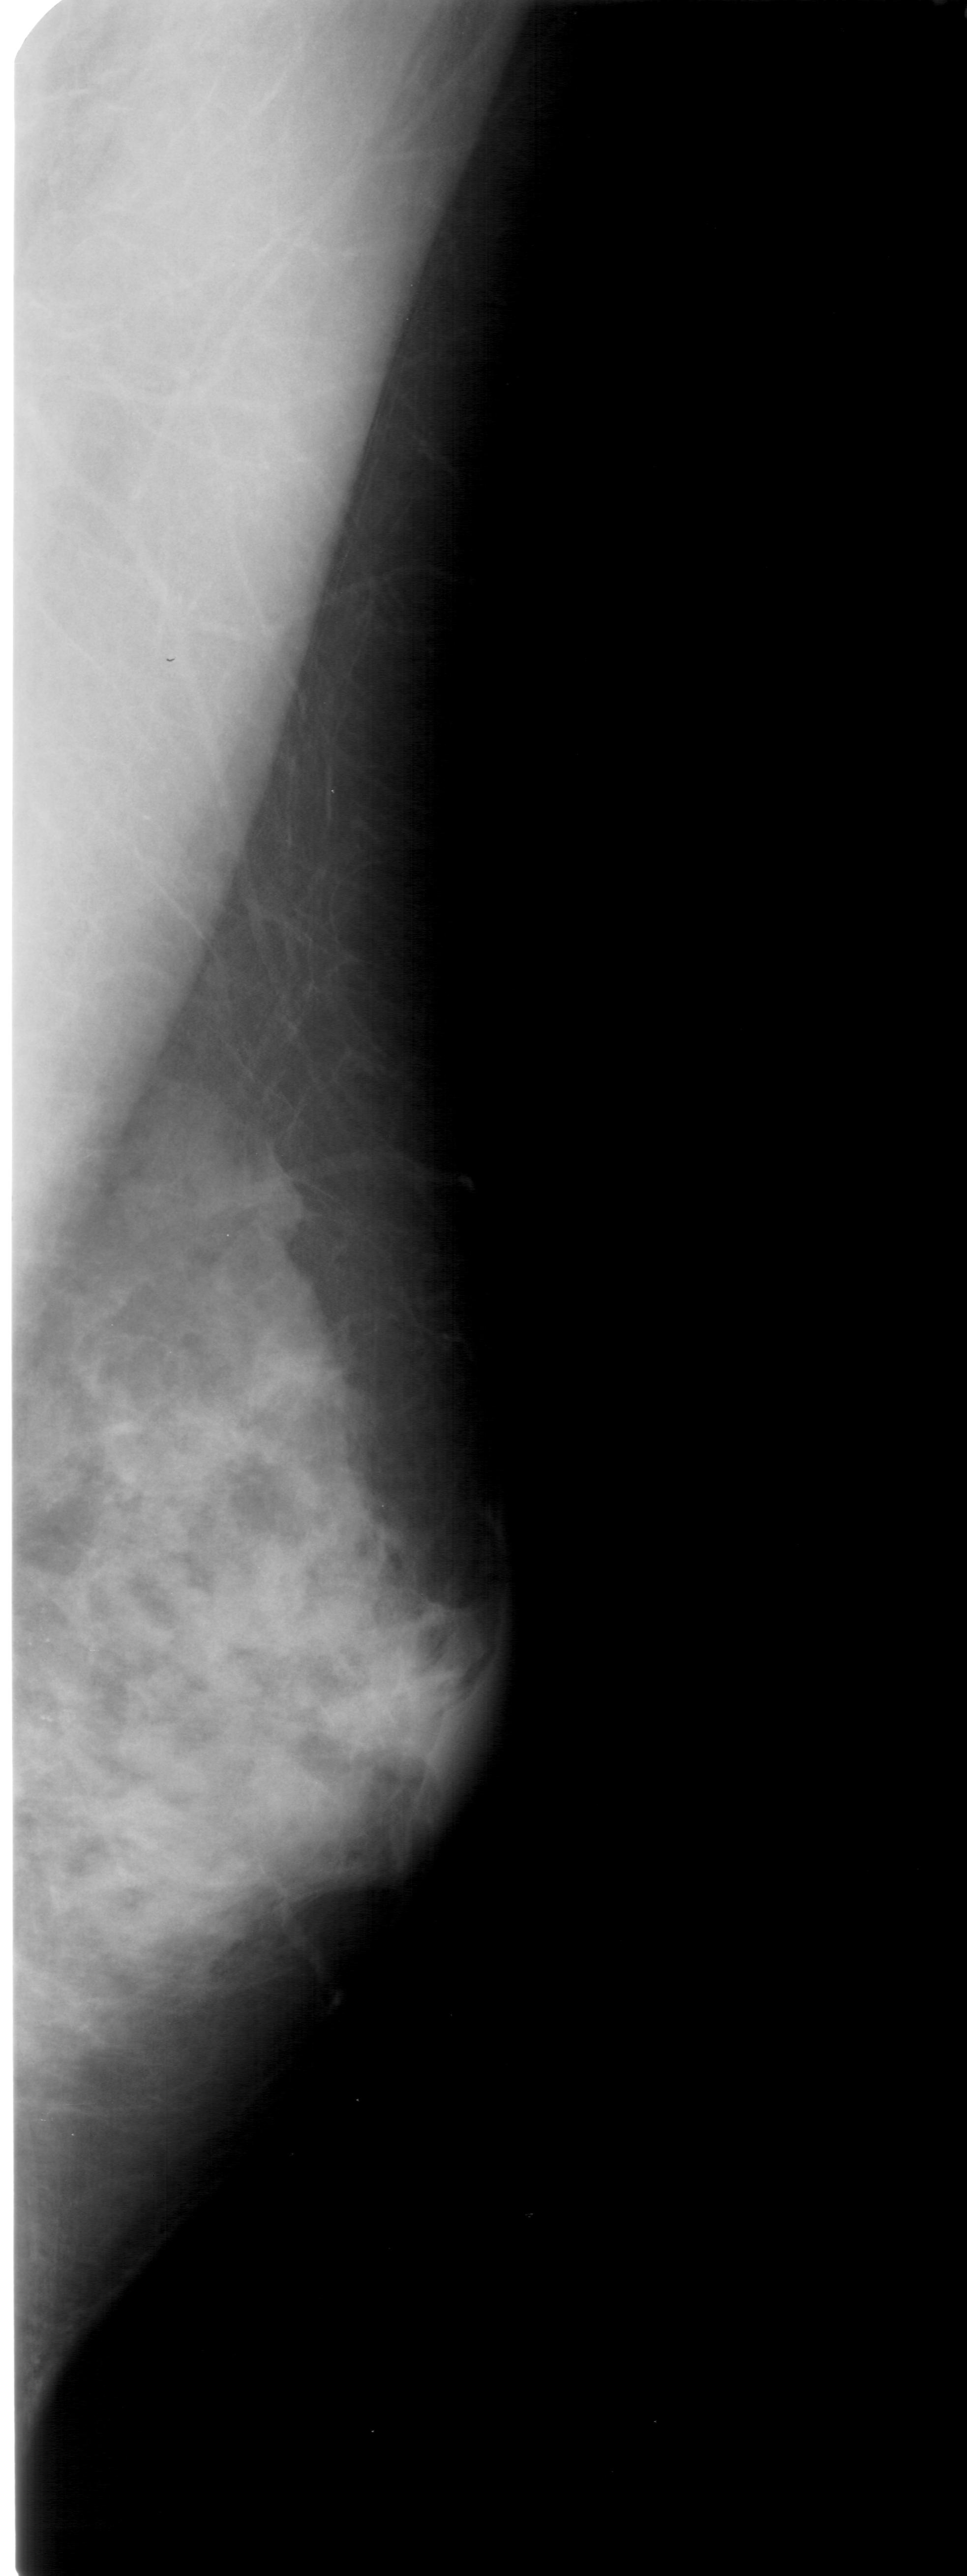
Mammogram (digitized film); right breast; mediolateral oblique (MLO) view; breast composition: extremely dense (BI-RADS density category 4 of 4); 967 × 2576 image matrix.
Expert-marked regions of interest on this film, with their recorded descriptors:
- calcifications, morphology pleomorphic, distribution clustered; BI-RADS assessment category 4; pathology result (as recorded, not read from the image): benign: bounding box [x1, y1, x2, y2] px = [29, 1612, 113, 1748]